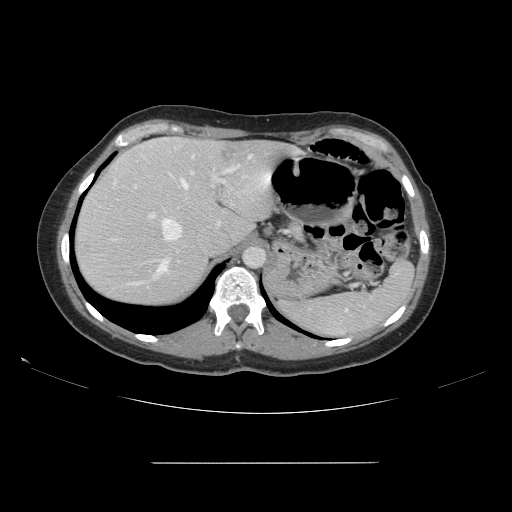
Contrast-enhanced abdominal CT, one axial slice; slice 116 of 151 in the series (ordered by position); 120 kVp; intravenous contrast given; soft-tissue window (W 400 / L 40 HU); 2.5 mm slice thickness; 512 × 512 image matrix. Female patient, age 46 years. From the clinical record (not read from this slice): diagnosis: colorectal cancer liver metastases, imaged before liver resection; multiple liver metastases: yes; largest metastasis: 3 cm; chemotherapy before resection: no.
Outlined on this slice (expert manual segmentation):
- hepatic veins: box from (x=149, y=154) to (x=253, y=241) px
- liver: (x=75, y=138)–(x=297, y=307)
- planned liver remnant (the part of the liver to remain after resection): (x=89, y=137)–(x=293, y=251)
- portal vein (with intrahepatic branches): (x=134, y=167)–(x=235, y=276)
- liver metastasis: (x=221, y=144)–(x=239, y=163)